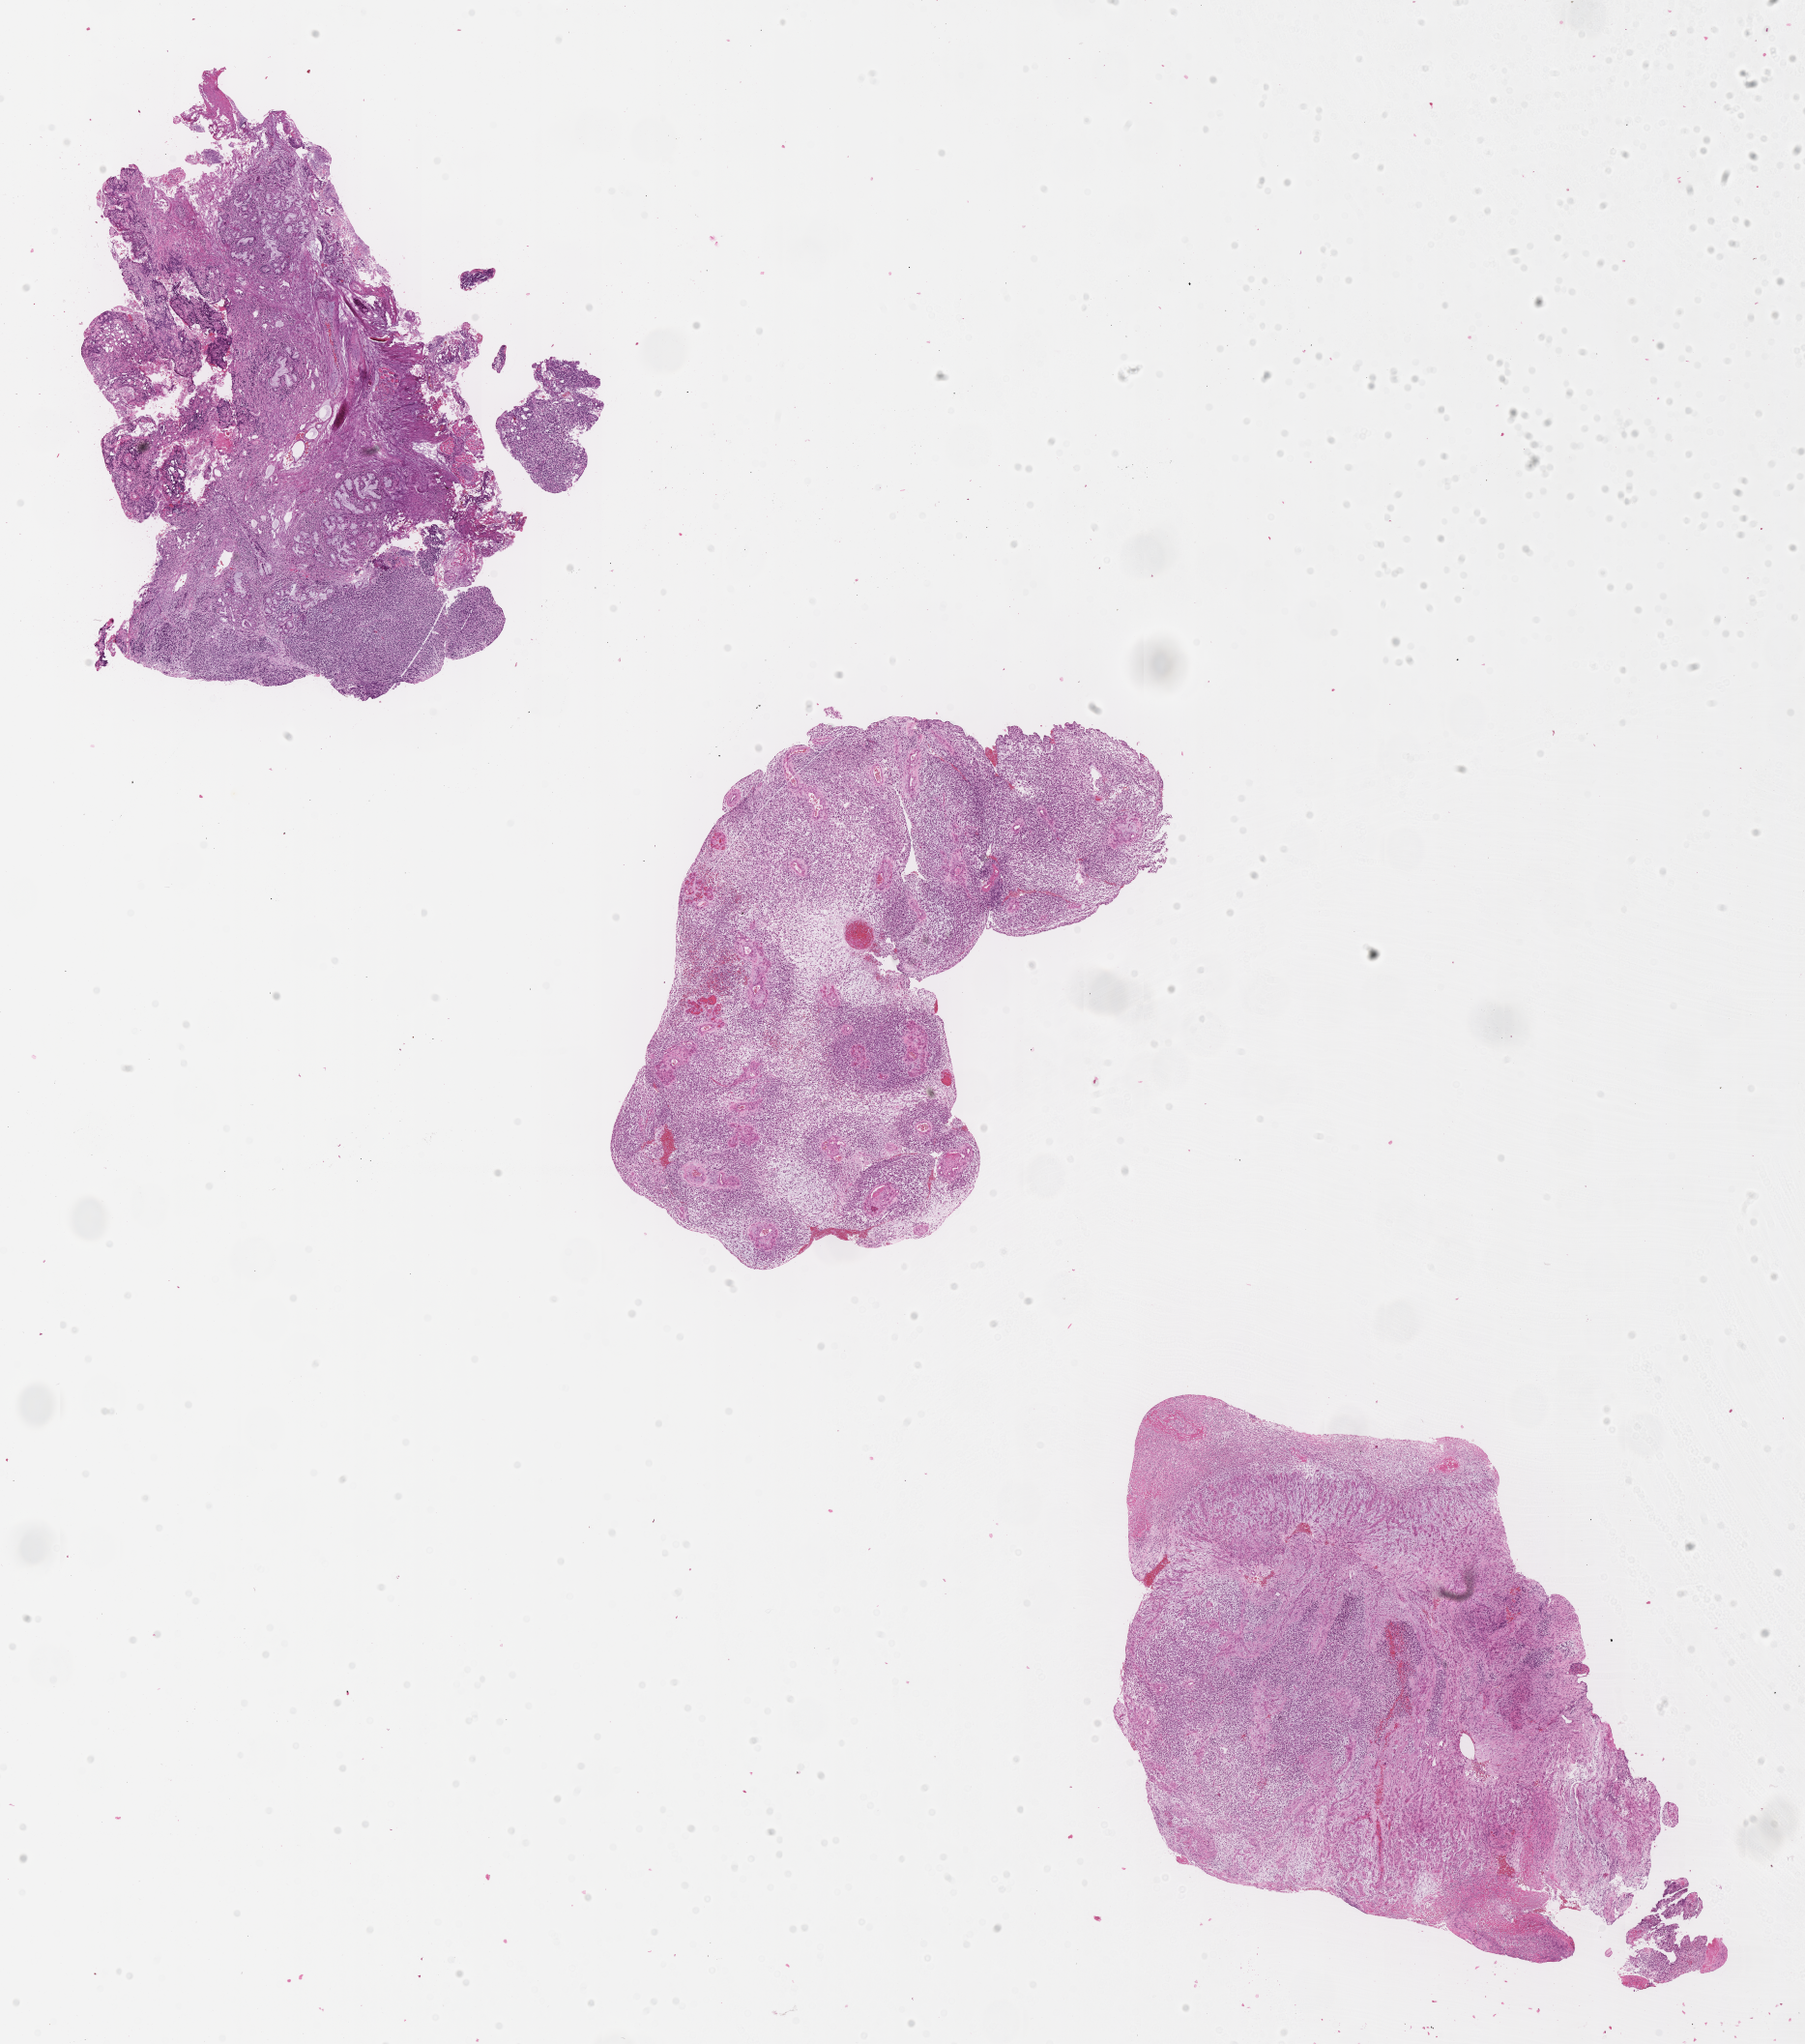
Haematoxylin and eosin whole-slide image of tumor tissue — whole scanned area (about 15.1 x 17.1 mm) shown as a low-resolution overview. Formalin-fixed paraffin-embedded section. Site: nasopharynx. Male patient, age at diagnosis 7.4 years.
Stage (as recorded): 3. Diagnosis: rhabdomyosarcoma; histological classification: embryonal rhabdomyosarcoma.